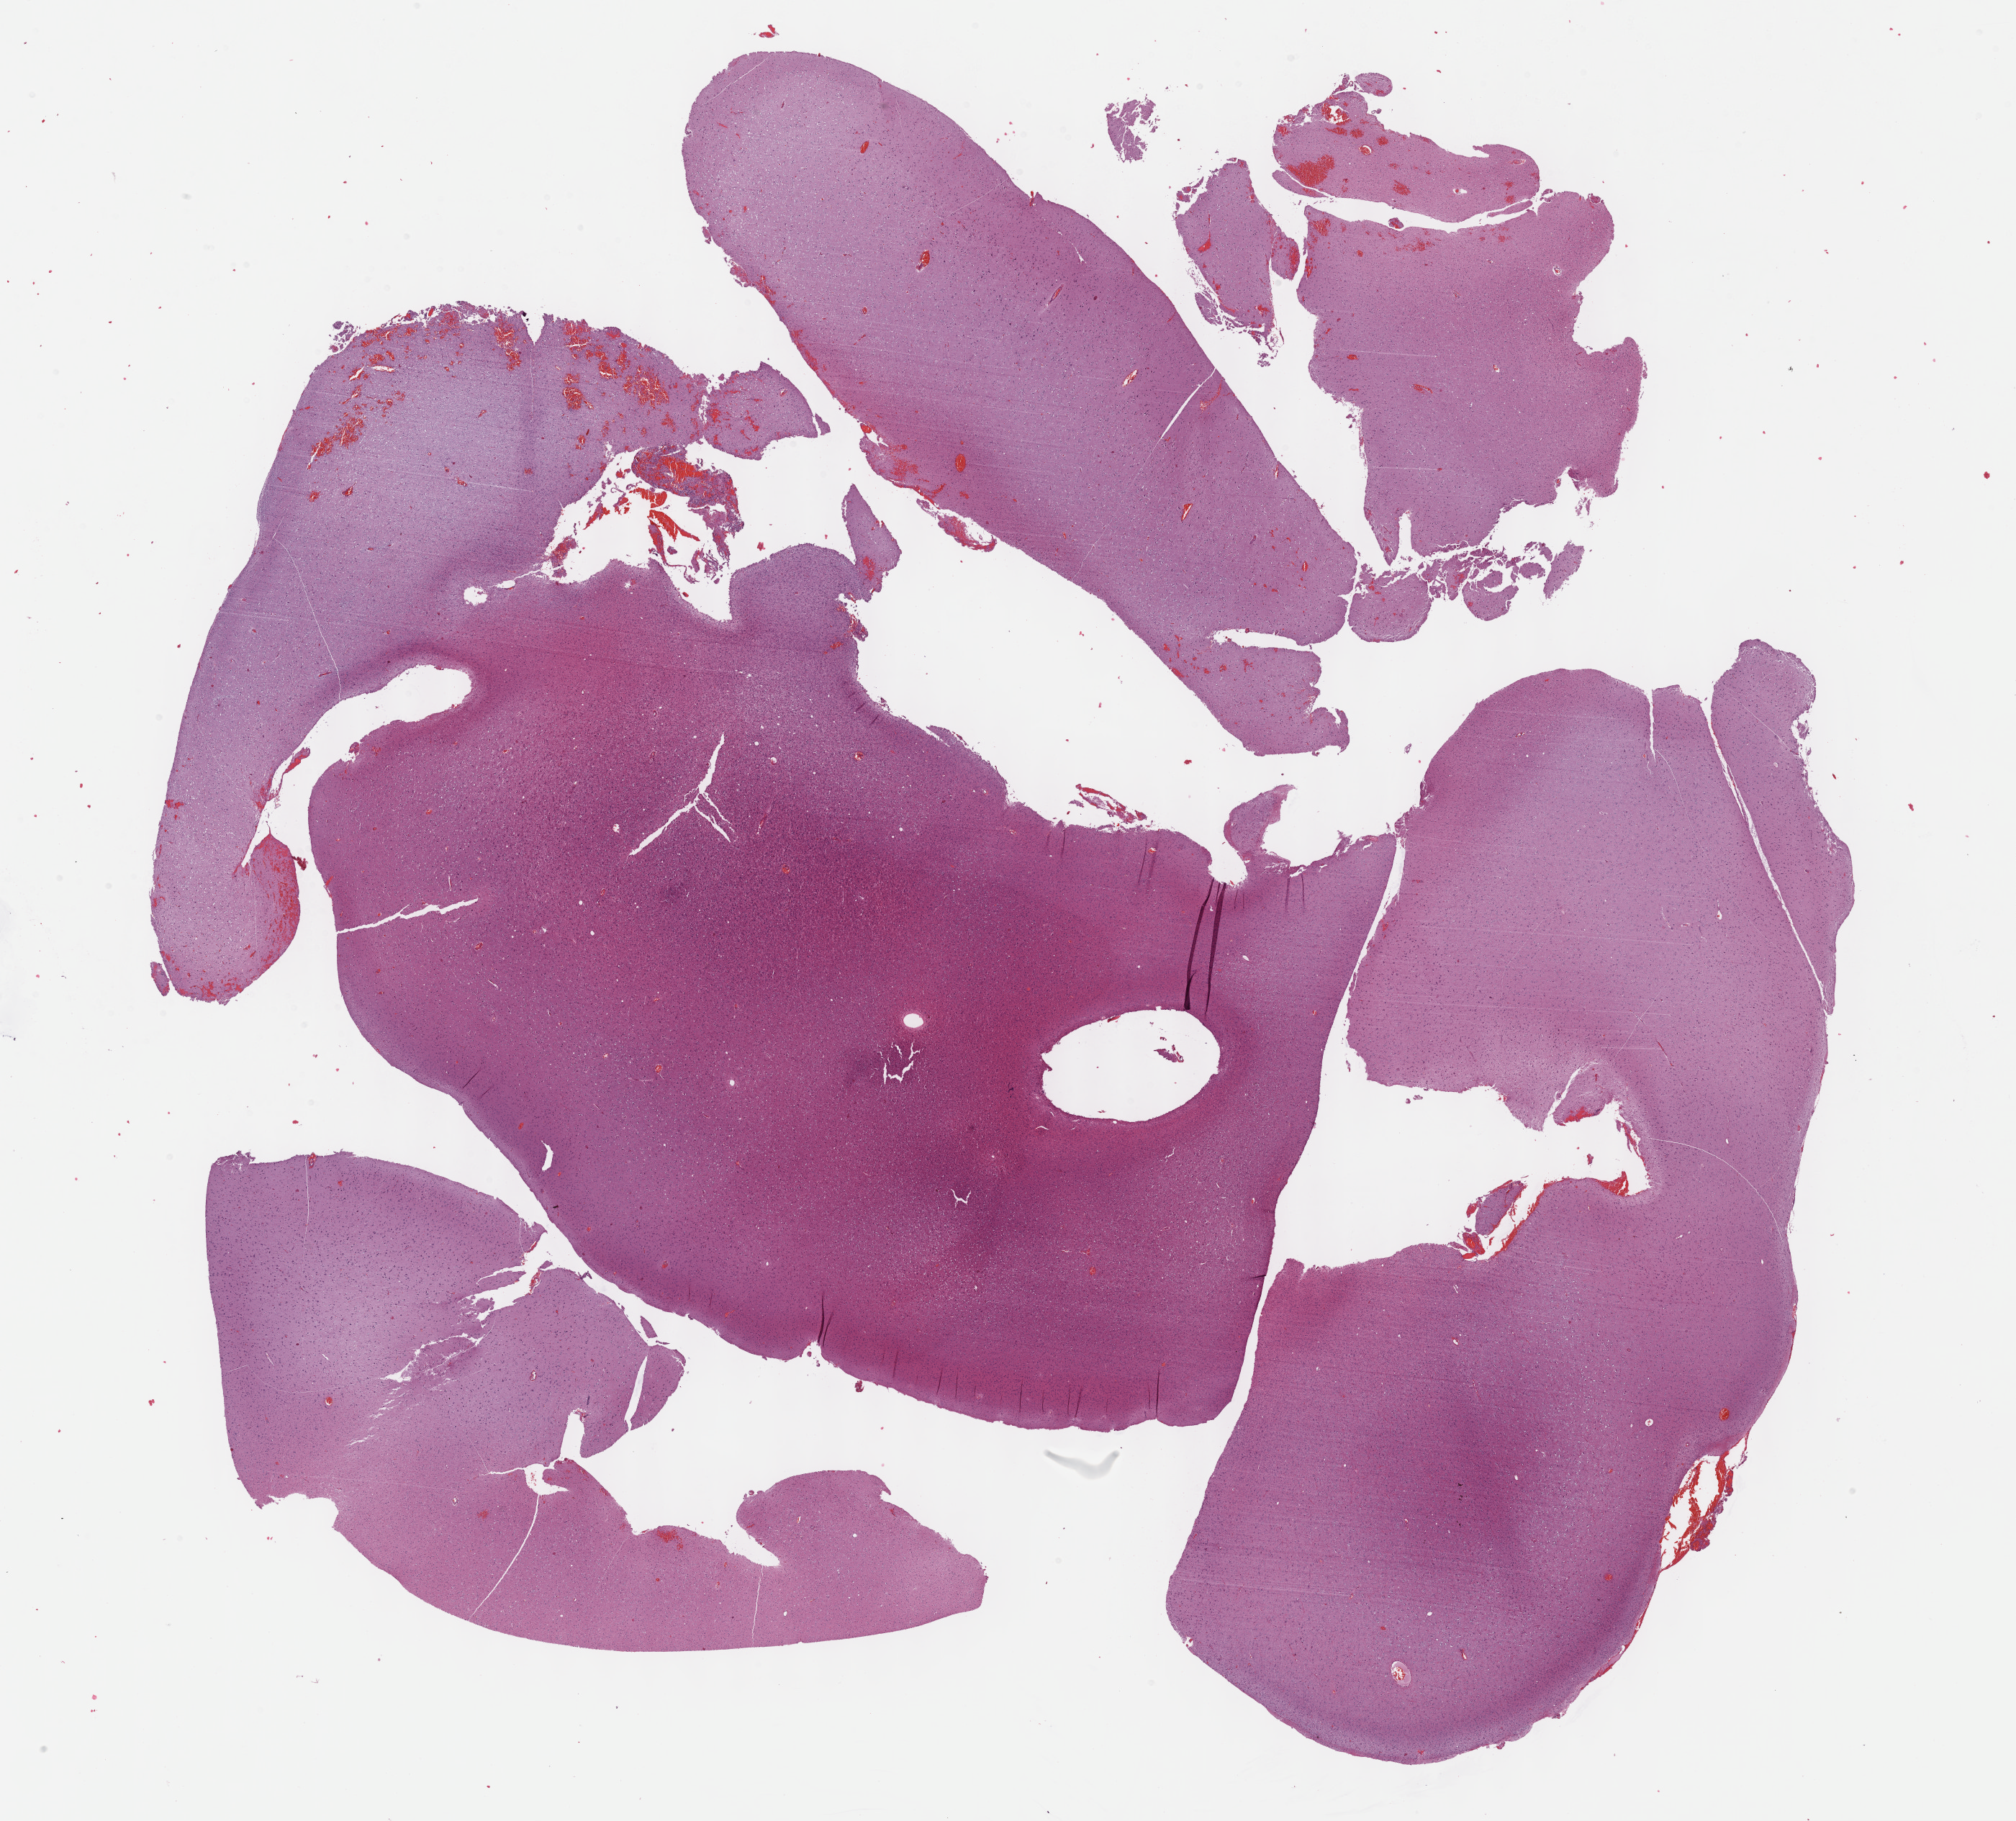
H&E-stained whole-slide image, whole scanned area (about 22.7 x 20.5 mm) shown as a low-resolution overview. Formalin-fixed paraffin-embedded (FFPE) diagnostic section. Sample: primary tumour, brain. Male patient; age at initial diagnosis 38 years. Histologic grade: G2 (moderately differentiated).
• laterality: right
• diagnosis: Oligodendroglioma, NOS